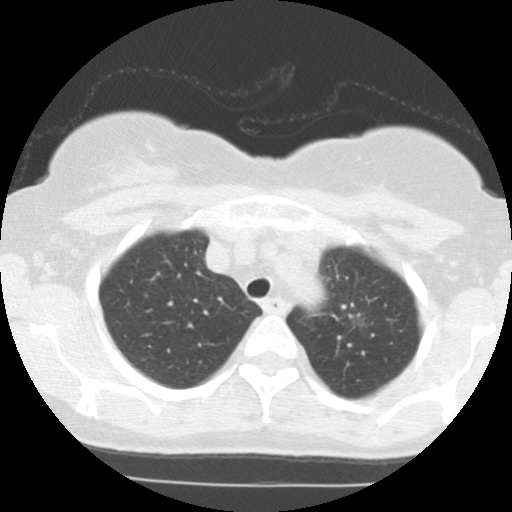
Axial slice from a low-dose chest CT screening exam, baseline screening round, lung window (W 1500 / L -600 HU), standard (soft-tissue) reconstruction kernel (STANDARD), slice 98 of 123 in the series, 512 × 512 image matrix, field of view 290 × 290 mm. Female participant, aged 61 years at enrolment.
Expert reader's lesion annotation, bounding box (x1, y1, x2, y2) in pixels: (319, 295, 391, 350). The screening reader recorded 2 non-calcified nodules or masses ≥4 mm on this exam (right lower lobe, left upper lobe); which of them this box marks is not recorded.